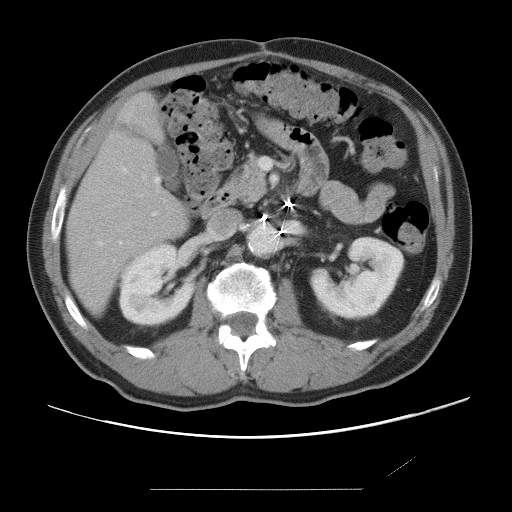
Contrast-enhanced abdominal CT, one axial slice. 120 kVp. Intravenous contrast given. Soft-tissue window (W 400 / L 40 HU). 512 × 512 image matrix. Male patient, age 74 years. Case-level facts recorded for this patient, not image findings: diagnosis: colorectal cancer liver metastases, imaged before liver resection; multiple liver metastases: yes; largest metastasis: 1.1 cm; chemotherapy before resection: yes.
Annotated regions visible in this slice (manually delineated by an expert):
- hepatic veins: bounding box [x1, y1, x2, y2] px = [99, 168, 159, 246]
- liver: [67, 96, 187, 311]
- planned liver remnant (the part of the liver to remain after resection): [68, 96, 187, 311]
- portal vein (with intrahepatic branches): [143, 177, 157, 215]
- liver metastasis: [75, 258, 83, 268]